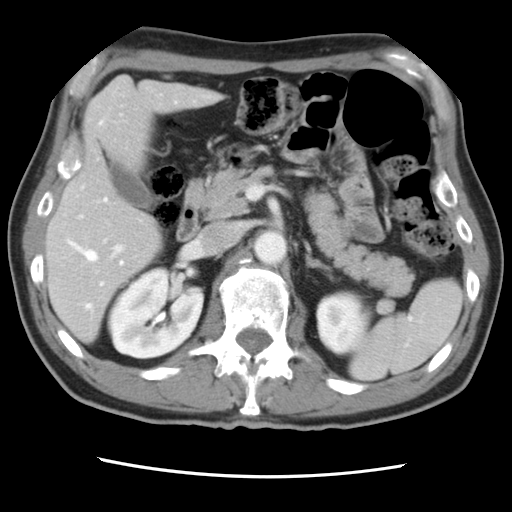
Contrast-enhanced abdominal CT, one axial slice; slice 43 of 83 in the series (ordered by position); 120 kVp; intravenous contrast given; soft-tissue window (W 400 / L 40 HU); 5 mm slice thickness; 512 × 512 image matrix, field of view 321 × 321 mm. Male patient, age 69 years. Case-level facts recorded for this patient, not image findings: diagnosis: colorectal cancer liver metastases, imaged before liver resection; multiple liver metastases: yes; largest metastasis: 3.5 cm; disease in both lobes: no.
Annotated regions visible in this slice (manually delineated by an expert):
- hepatic veins: bounding box <68,121,124,309> (left, top, right, bottom; pixels)
- liver: <48,78,219,340>
- planned liver remnant (the part of the liver to remain after resection): <48,148,163,341>
- portal vein (with intrahepatic branches): <78,185,125,272>